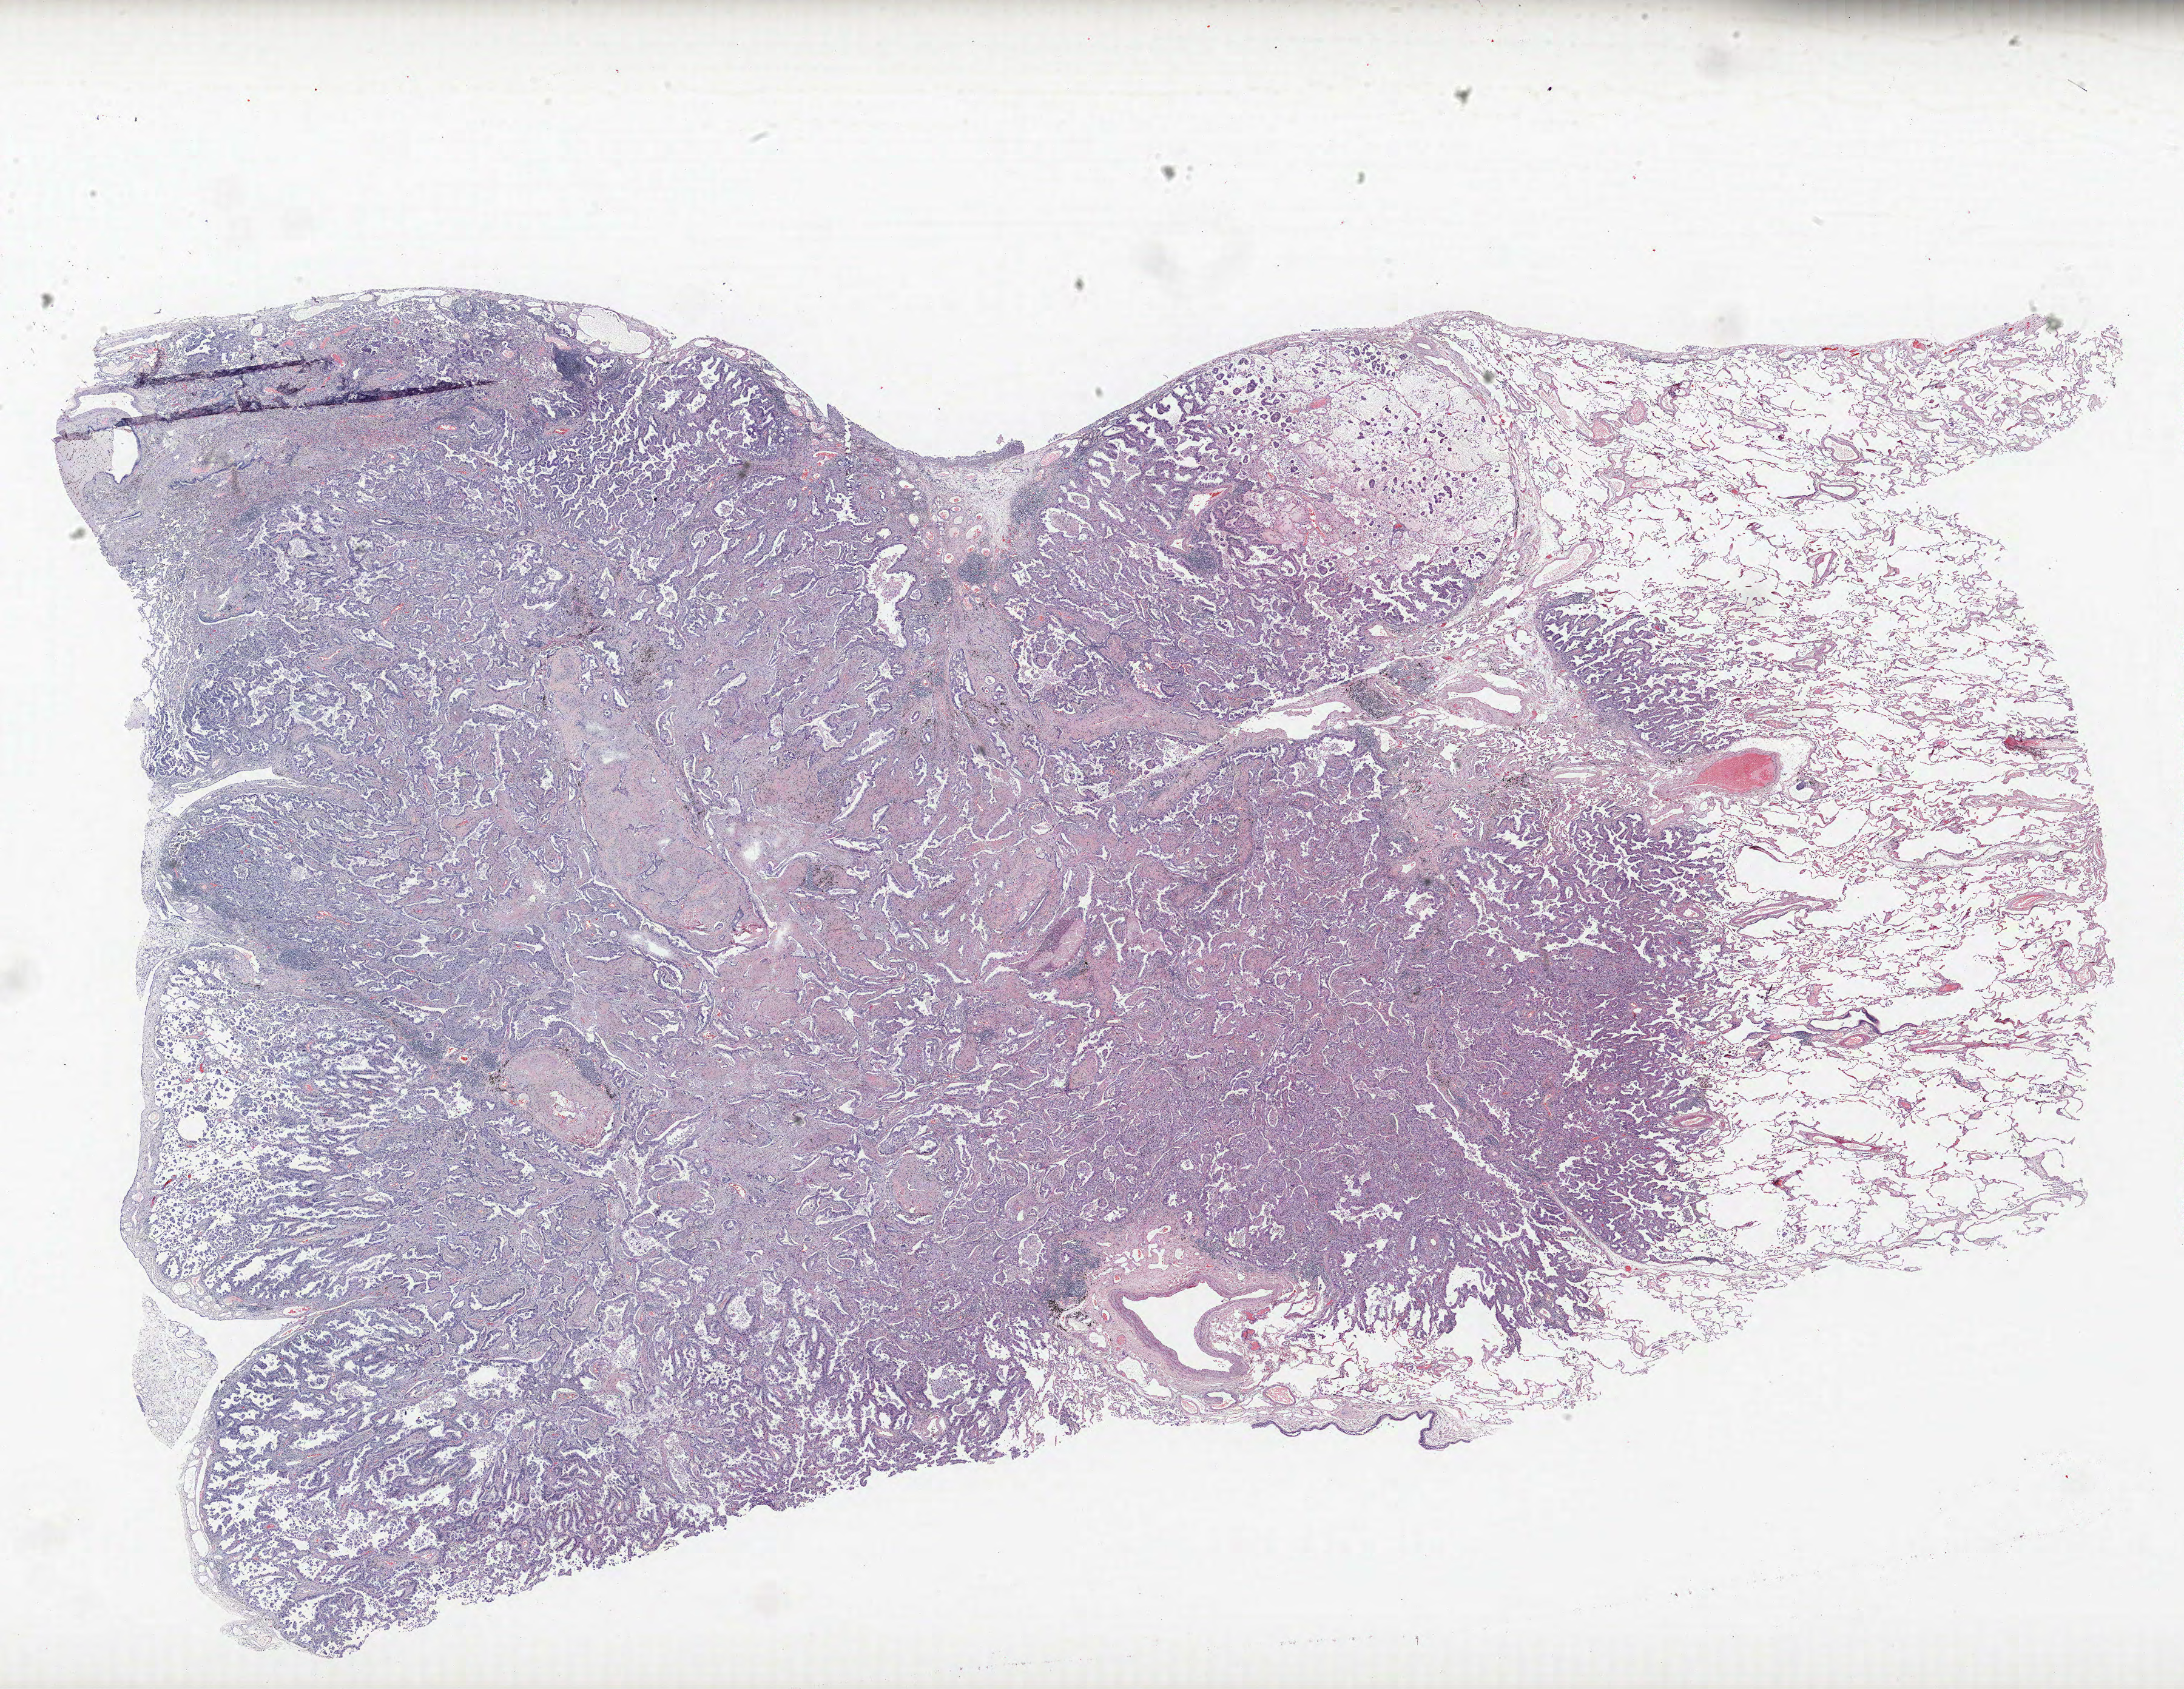
Hematoxylin and eosin (H&E) stained whole-slide image, a low-resolution overview of the entire scanned area, about 28.8 x 22.3 mm (from a 40x scan), FFPE section, lung. Male, age 65 at enrolment. Current smoker at enrolment.
Participant's lung-cancer diagnosis: Adenocarcinoma, NOS (ICD-O-3 8140/3).